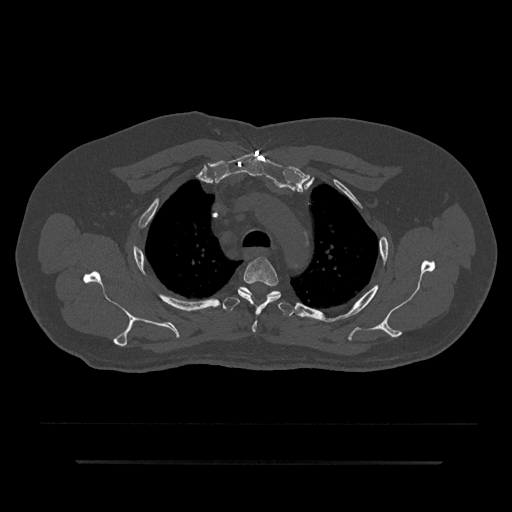
CT including the spine, one axial slice. Slice 645 of 797 in the series (ordered by position). Reconstruction kernel Br40s/3. 120 kVp. Bone window (W 1800 / L 400 HU). 0.5 mm slice thickness. 512 × 512 image matrix, field of view 464 × 464 mm. Male patient, age 59 years. From the clinical record (not read from this slice): primary cancer: bile ducts; vertebrae with lytic lesions (as recorded): T10.
Structures marked on this image (semi-automatically segmented with operator editing):
- T3 vertebra: bounding box (x1, y1, x2, y2) in pixels: (238, 257, 281, 332)
- T4 vertebra: (222, 287, 294, 316)